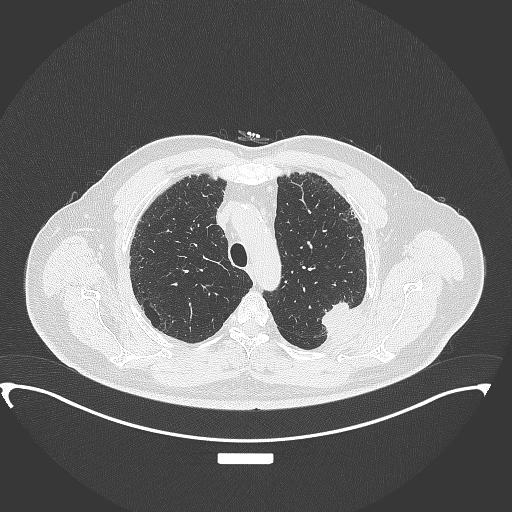
Chest CT, one axial slice; slice 280 of 350 in the series (ordered by position); 120 kVp; lung window (W 1500 / L -600 HU); 1 mm slice thickness; 512 × 512 image matrix, field of view 459 × 459 mm. Patient: male, 64 years. From the clinical record (not read from this slice): clinical TNM (as recorded): T1c N1 M1.
Outlined on this slice (bounding box drawn by a radiologist):
- lung tumour (recorded histology: adenocarcinoma): bounding box <321,300,362,342> (left, top, right, bottom; pixels)